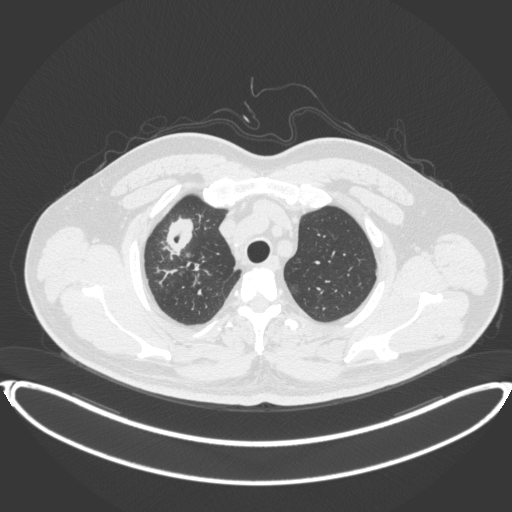
Chest CT, one axial slice. Reconstruction kernel B31f. 120 kVp. Lung window (W 1500 / L -600 HU). 1 mm slice thickness. 512 × 512 image matrix, field of view 445 × 445 mm. Patient: male, 53 years. Case-level facts recorded for this patient, not image findings: clinical TNM (as recorded): T2a N0 M0.
Outlined on this slice (bounding box drawn by a radiologist):
- lung tumour (recorded histology: adenocarcinoma): bounding box (x1, y1, x2, y2) in pixels: (160, 213, 201, 262)